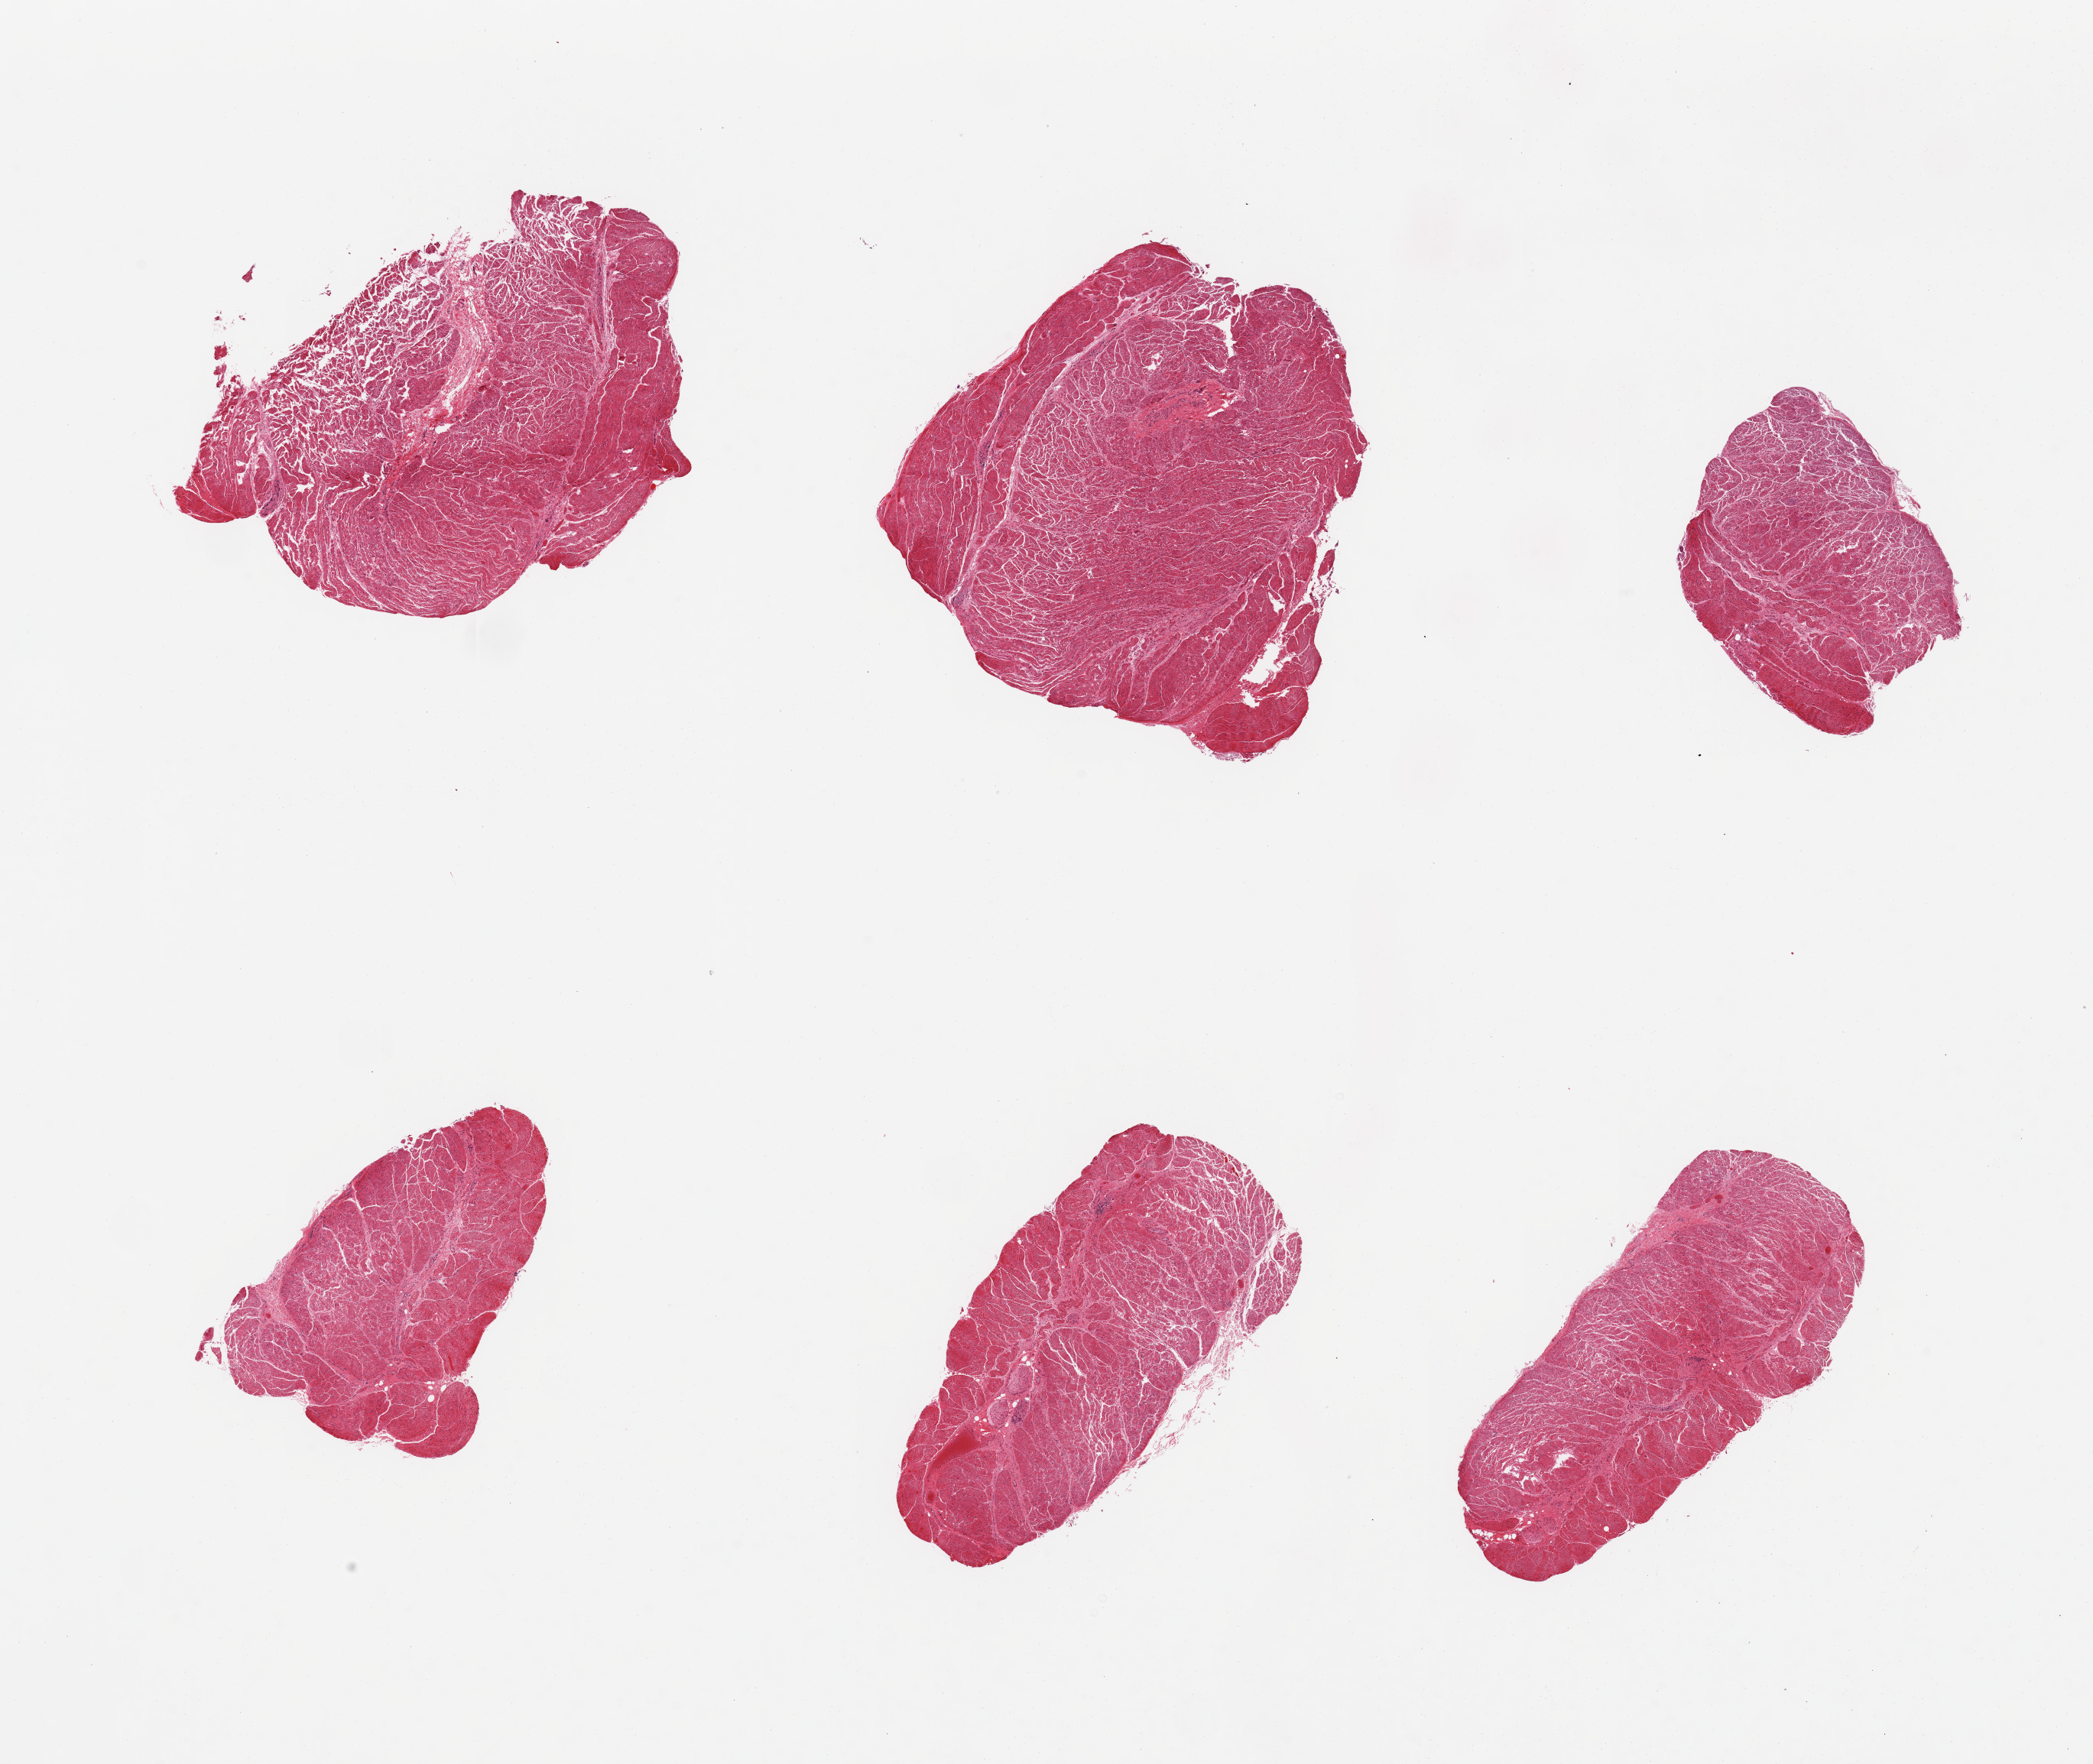
Digitized H&E-stained section, whole scanned area (about 21.7 x 18.3 mm, slide scanned at 20x) shown as a low-resolution overview; PAXgene-fixed paraffin-embedded (PFPE) section; sampled site (target tissue): gastroesophageal junction; tissue donor sample. Donor: male.
Reviewer comment on this tissue sample: 6 pieces; well trimmed muscularis.